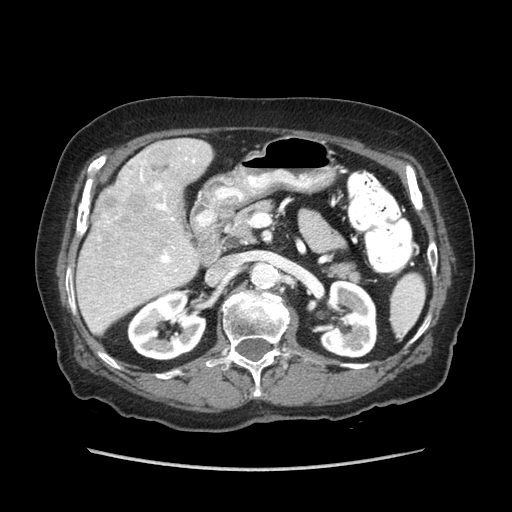
Contrast-enhanced abdominal CT (liver protocol), one axial slice; position 35 of 89 along the scan axis; reconstruction kernel STANDARD; 140 kVp; soft-tissue window (W 400 / L 40 HU); 512 × 512 image matrix, field of view 360 × 360 mm. From the clinical record (not read from this slice): diagnosis: hepatocellular carcinoma (patient treated with transarterial chemoembolisation; whether this scan precedes or follows treatment is not stated here); TNM stage (as recorded): Stage-IIIA; Child-Pugh class: A; tumour differentiation: well differentiated; tumour nodularity: multinodular.
Outlined on this slice (semi-automatically segmented with operator editing):
- liver parenchyma outside the tumour (the mass and vessels are separate outlines, so this box may not span the whole liver): bounding box (x1, y1, x2, y2) in pixels: (76, 138, 212, 334)
- mass: (92, 144, 170, 232)
- liver vessels: (97, 148, 196, 320)